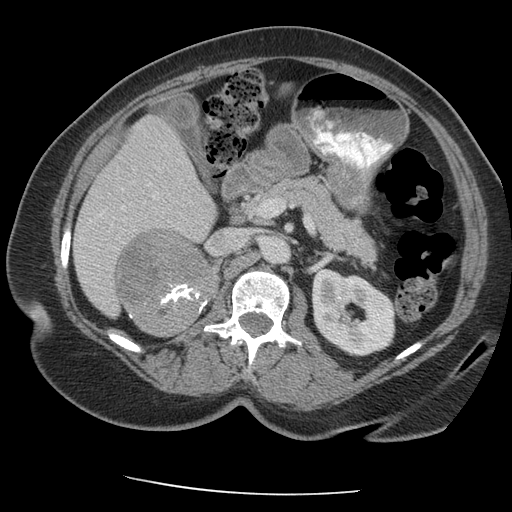
Contrast-enhanced abdominal CT, one axial slice. Slice 117 of 163 in the series (ordered by position). Reconstruction kernel STANDARD. 140 kVp. Intravenous contrast given. Soft-tissue window (W 400 / L 40 HU). 2.5 mm slice thickness. 512 × 512 image matrix, field of view 360 × 360 mm. Female patient, age 70 years. From the clinical record (not read from this slice): diagnosis: adrenocortical carcinoma; tumour side: right adrenal; tumour size at pathology: 9.5 cm.
Annotated regions visible in this slice (semi-automatic segmentation, software-assisted and operator-edited):
- mass: bounding box (x1, y1, x2, y2) in pixels: (117, 231, 217, 337)